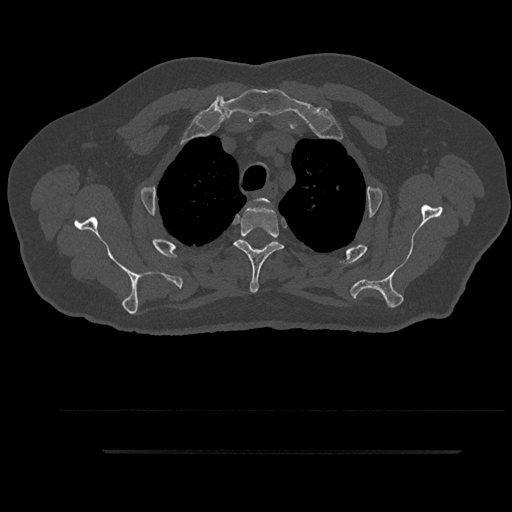
CT including the spine, one axial slice. Position 714 of 797 along the scan axis. 120 kVp. Bone window (W 1800 / L 400 HU). 0.5 mm slice thickness. 512 × 512 image matrix, field of view 432 × 432 mm. Male patient, age 63 years. From the clinical record (not read from this slice): primary cancer: renal; vertebrae with lytic lesions (as recorded): T8.
Structures marked on this image (semi-automatically segmented with operator editing):
- T2 vertebra: box from (x=254, y=198) to (x=271, y=205) px
- T3 vertebra: (x=234, y=205)–(x=284, y=293)